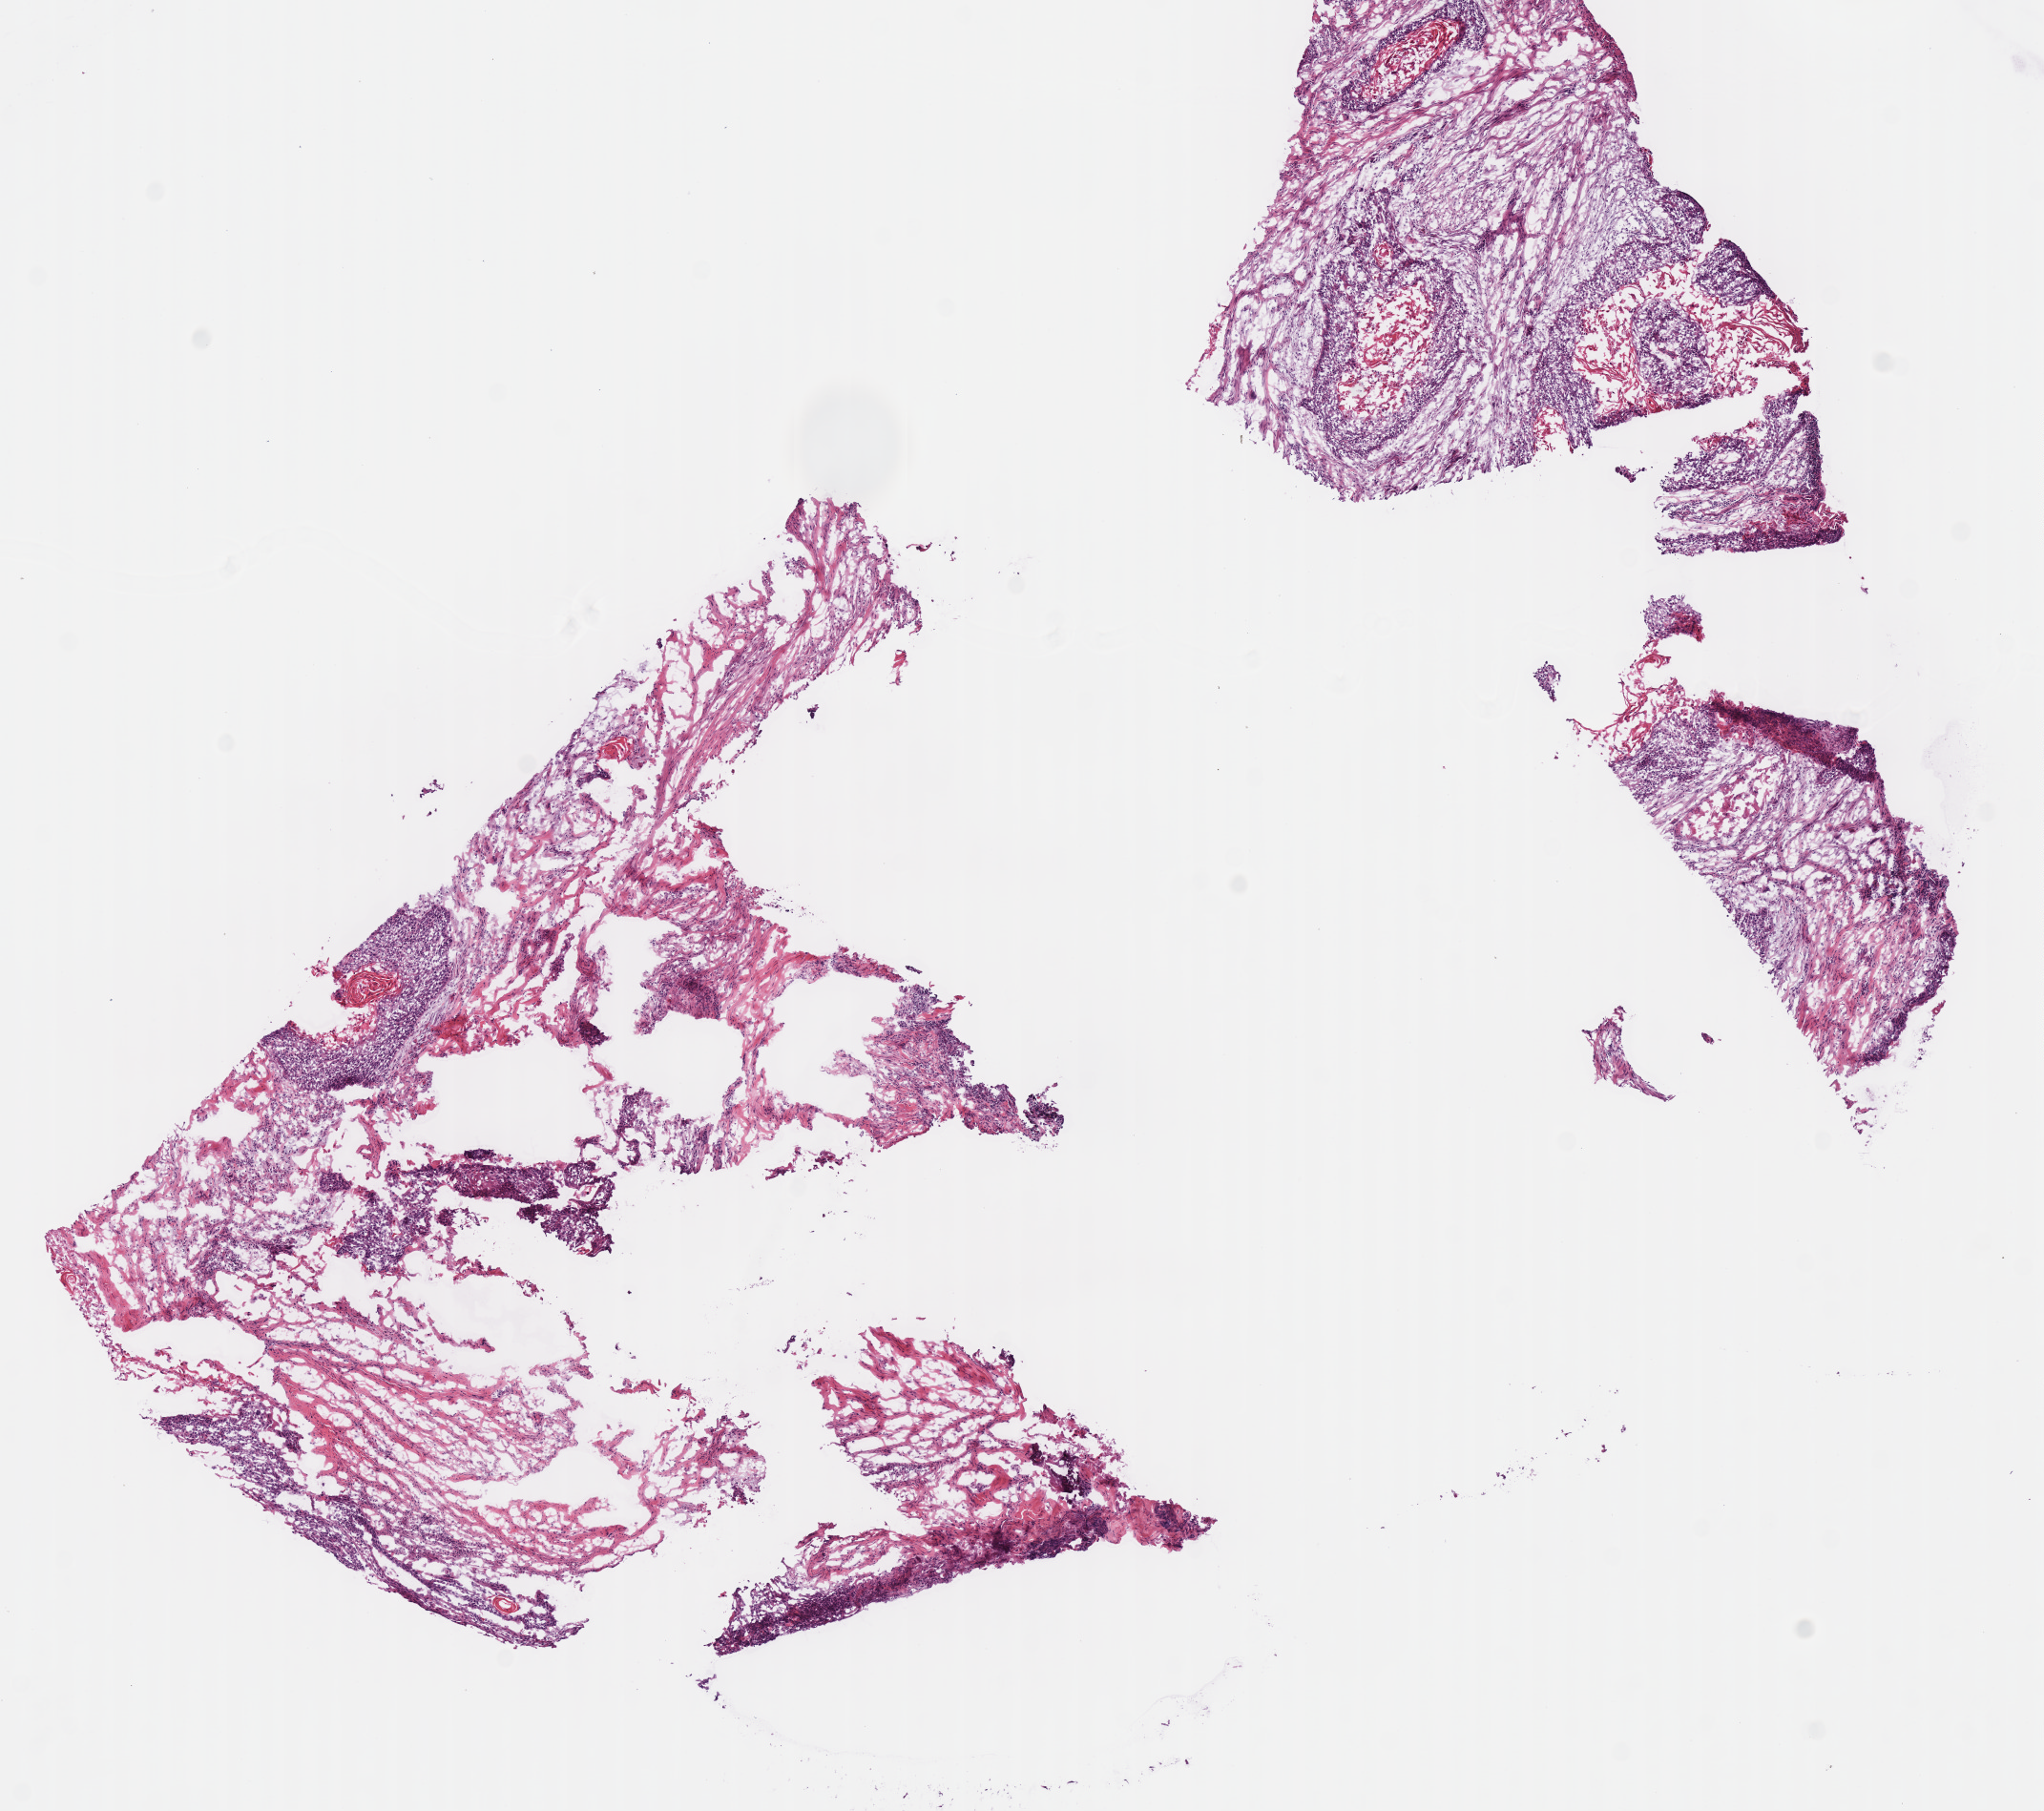
Hematoxylin and eosin (H&E) stained whole-slide image — low-resolution overview of the scanned area, about 8.4 x 7.5 mm (acquisition: 40x scan); frozen section; primary tumour sample from the head and neck. Female patient; age at initial diagnosis 57 years. Histologic grade: G2 (moderately differentiated). Pathologist review of this section (percent, as recorded): tumour cells 50%, tumour nuclei 60%, normal cells 0%, stromal cells 50%, necrosis 0%.
- pathologic diagnosis: Squamous cell carcinoma, NOS (overlapping lesion of lip, oral cavity and pharynx)
- AJCC pathologic stage: IVA (7th edition)